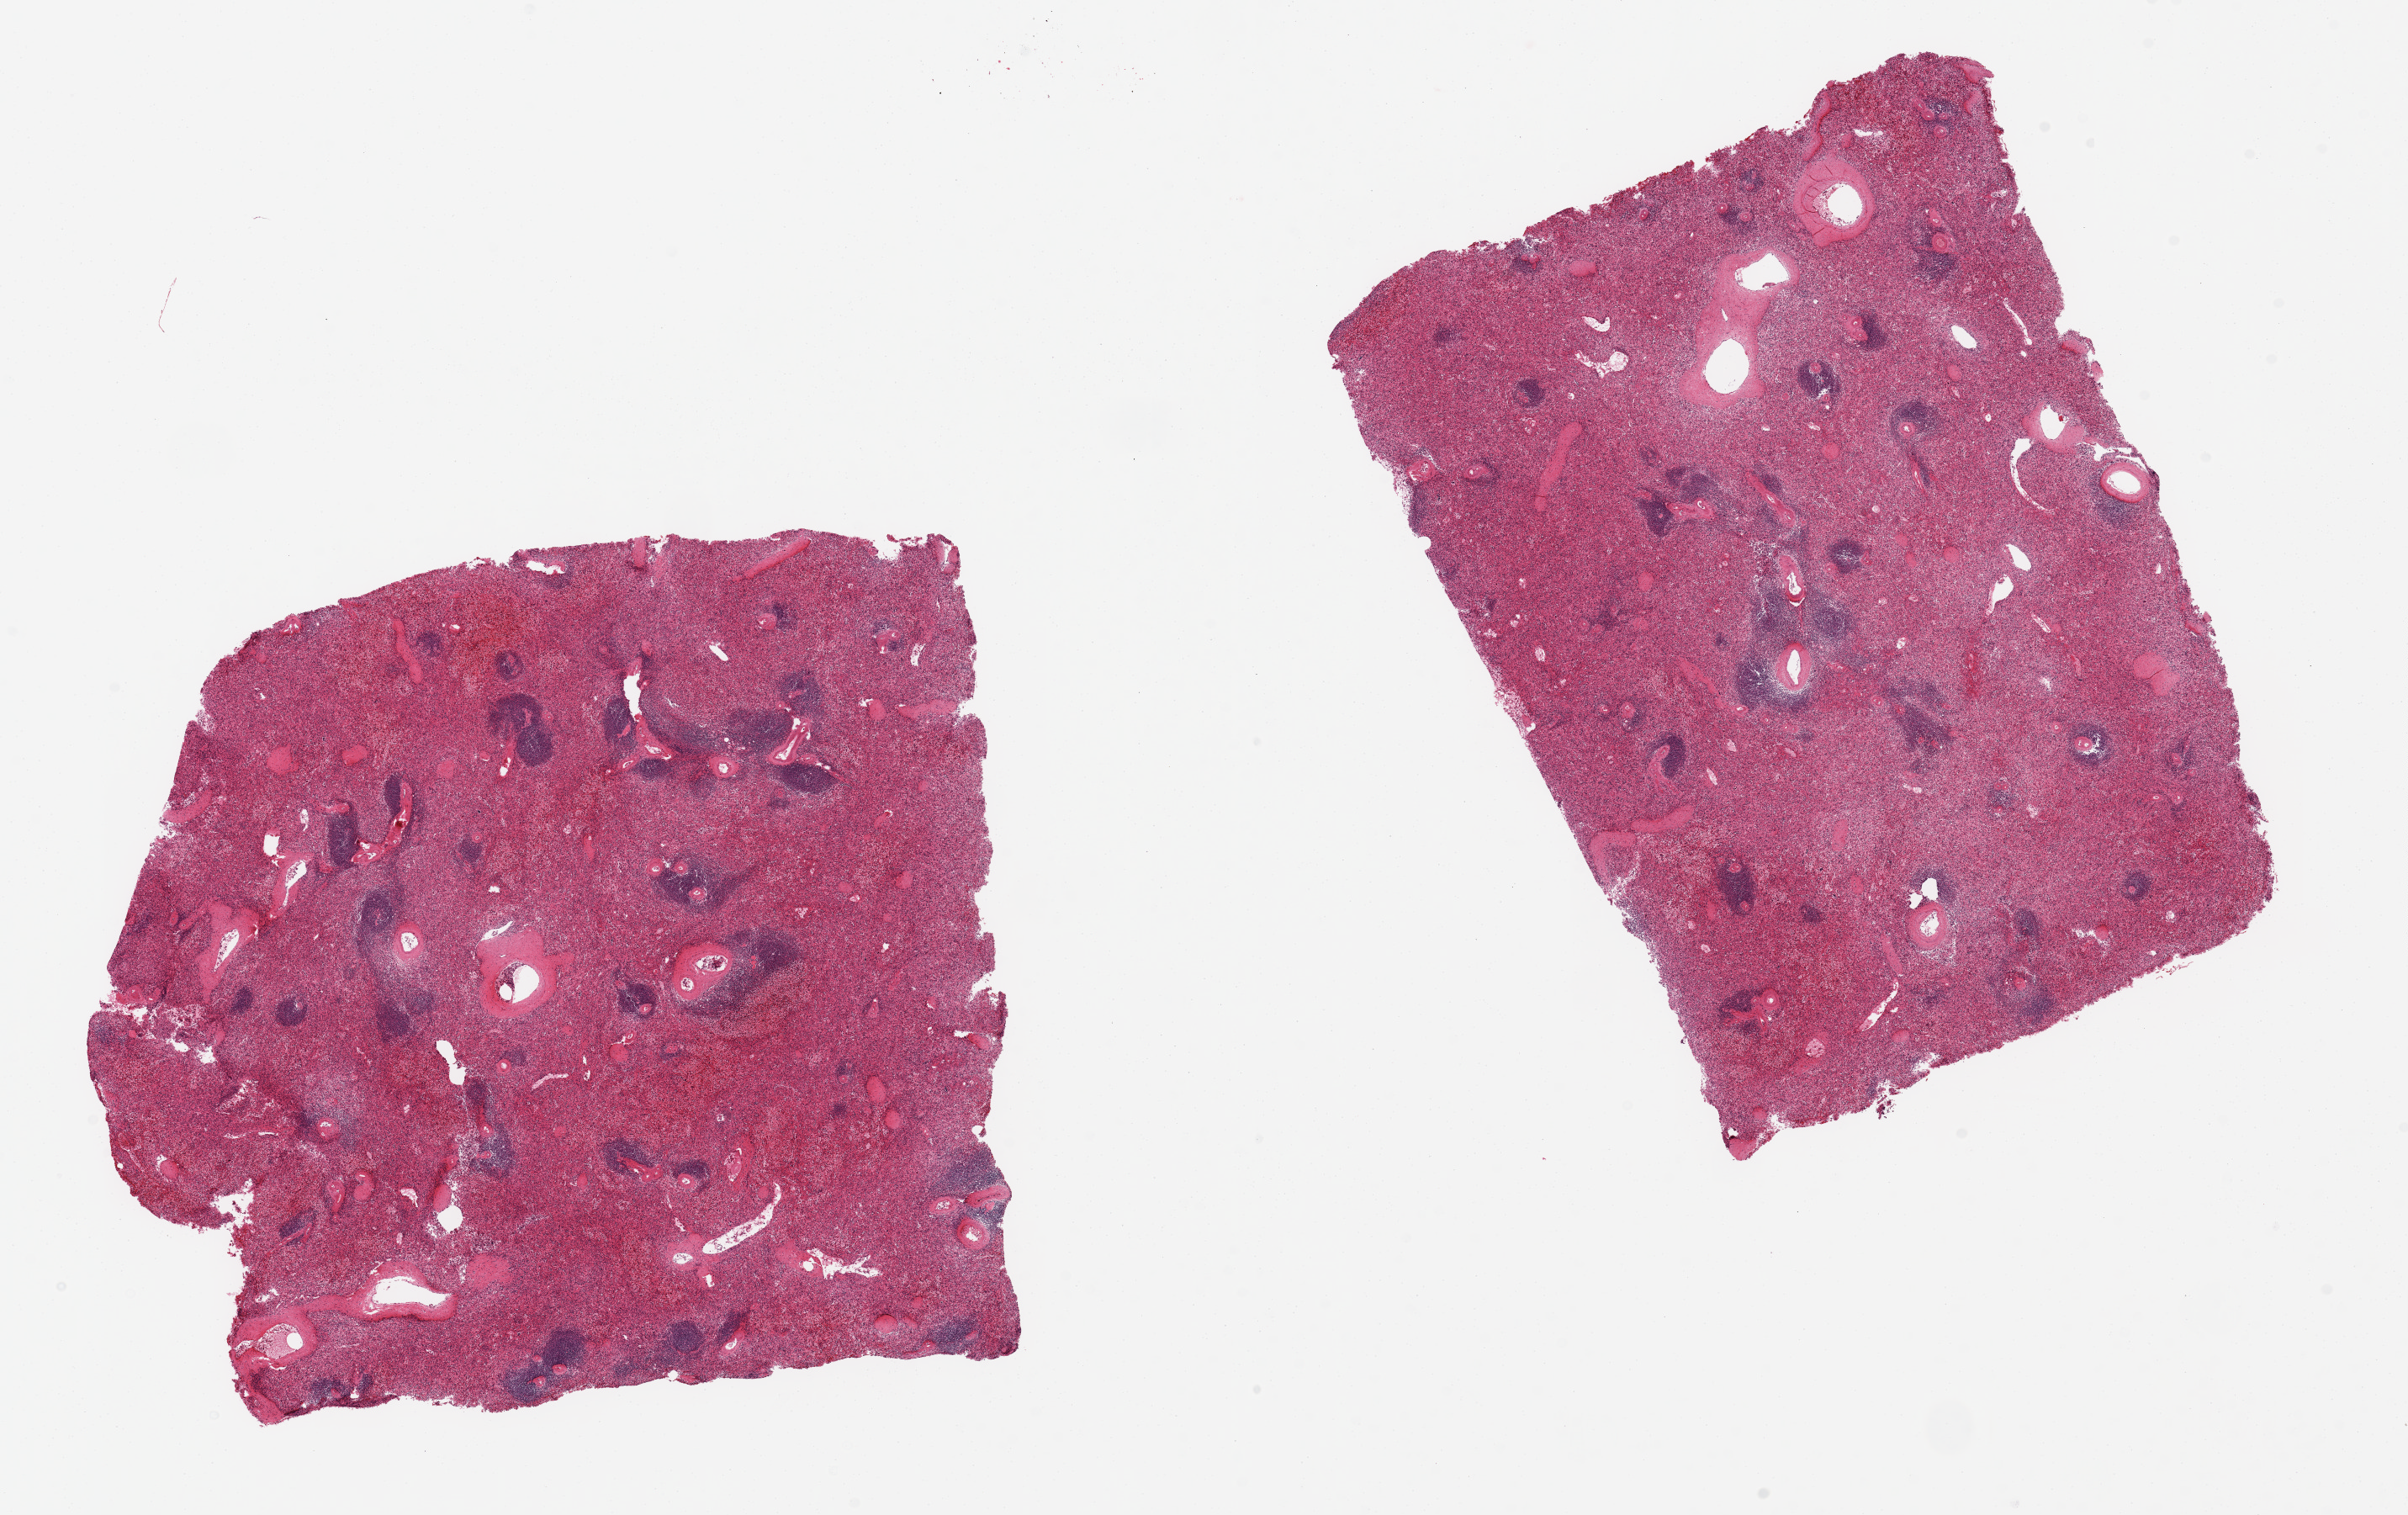
Haematoxylin and eosin whole-slide image — a low-resolution overview of the entire scanned area, about 22.6 x 14.2 mm; PAXgene-fixed, paraffin-embedded tissue; sampled site (target tissue): spleen; donor tissue sample. Donor: female.
Review note (as recorded): 2 ~ 7.5x7.5mm aliquots, red pulp congested.